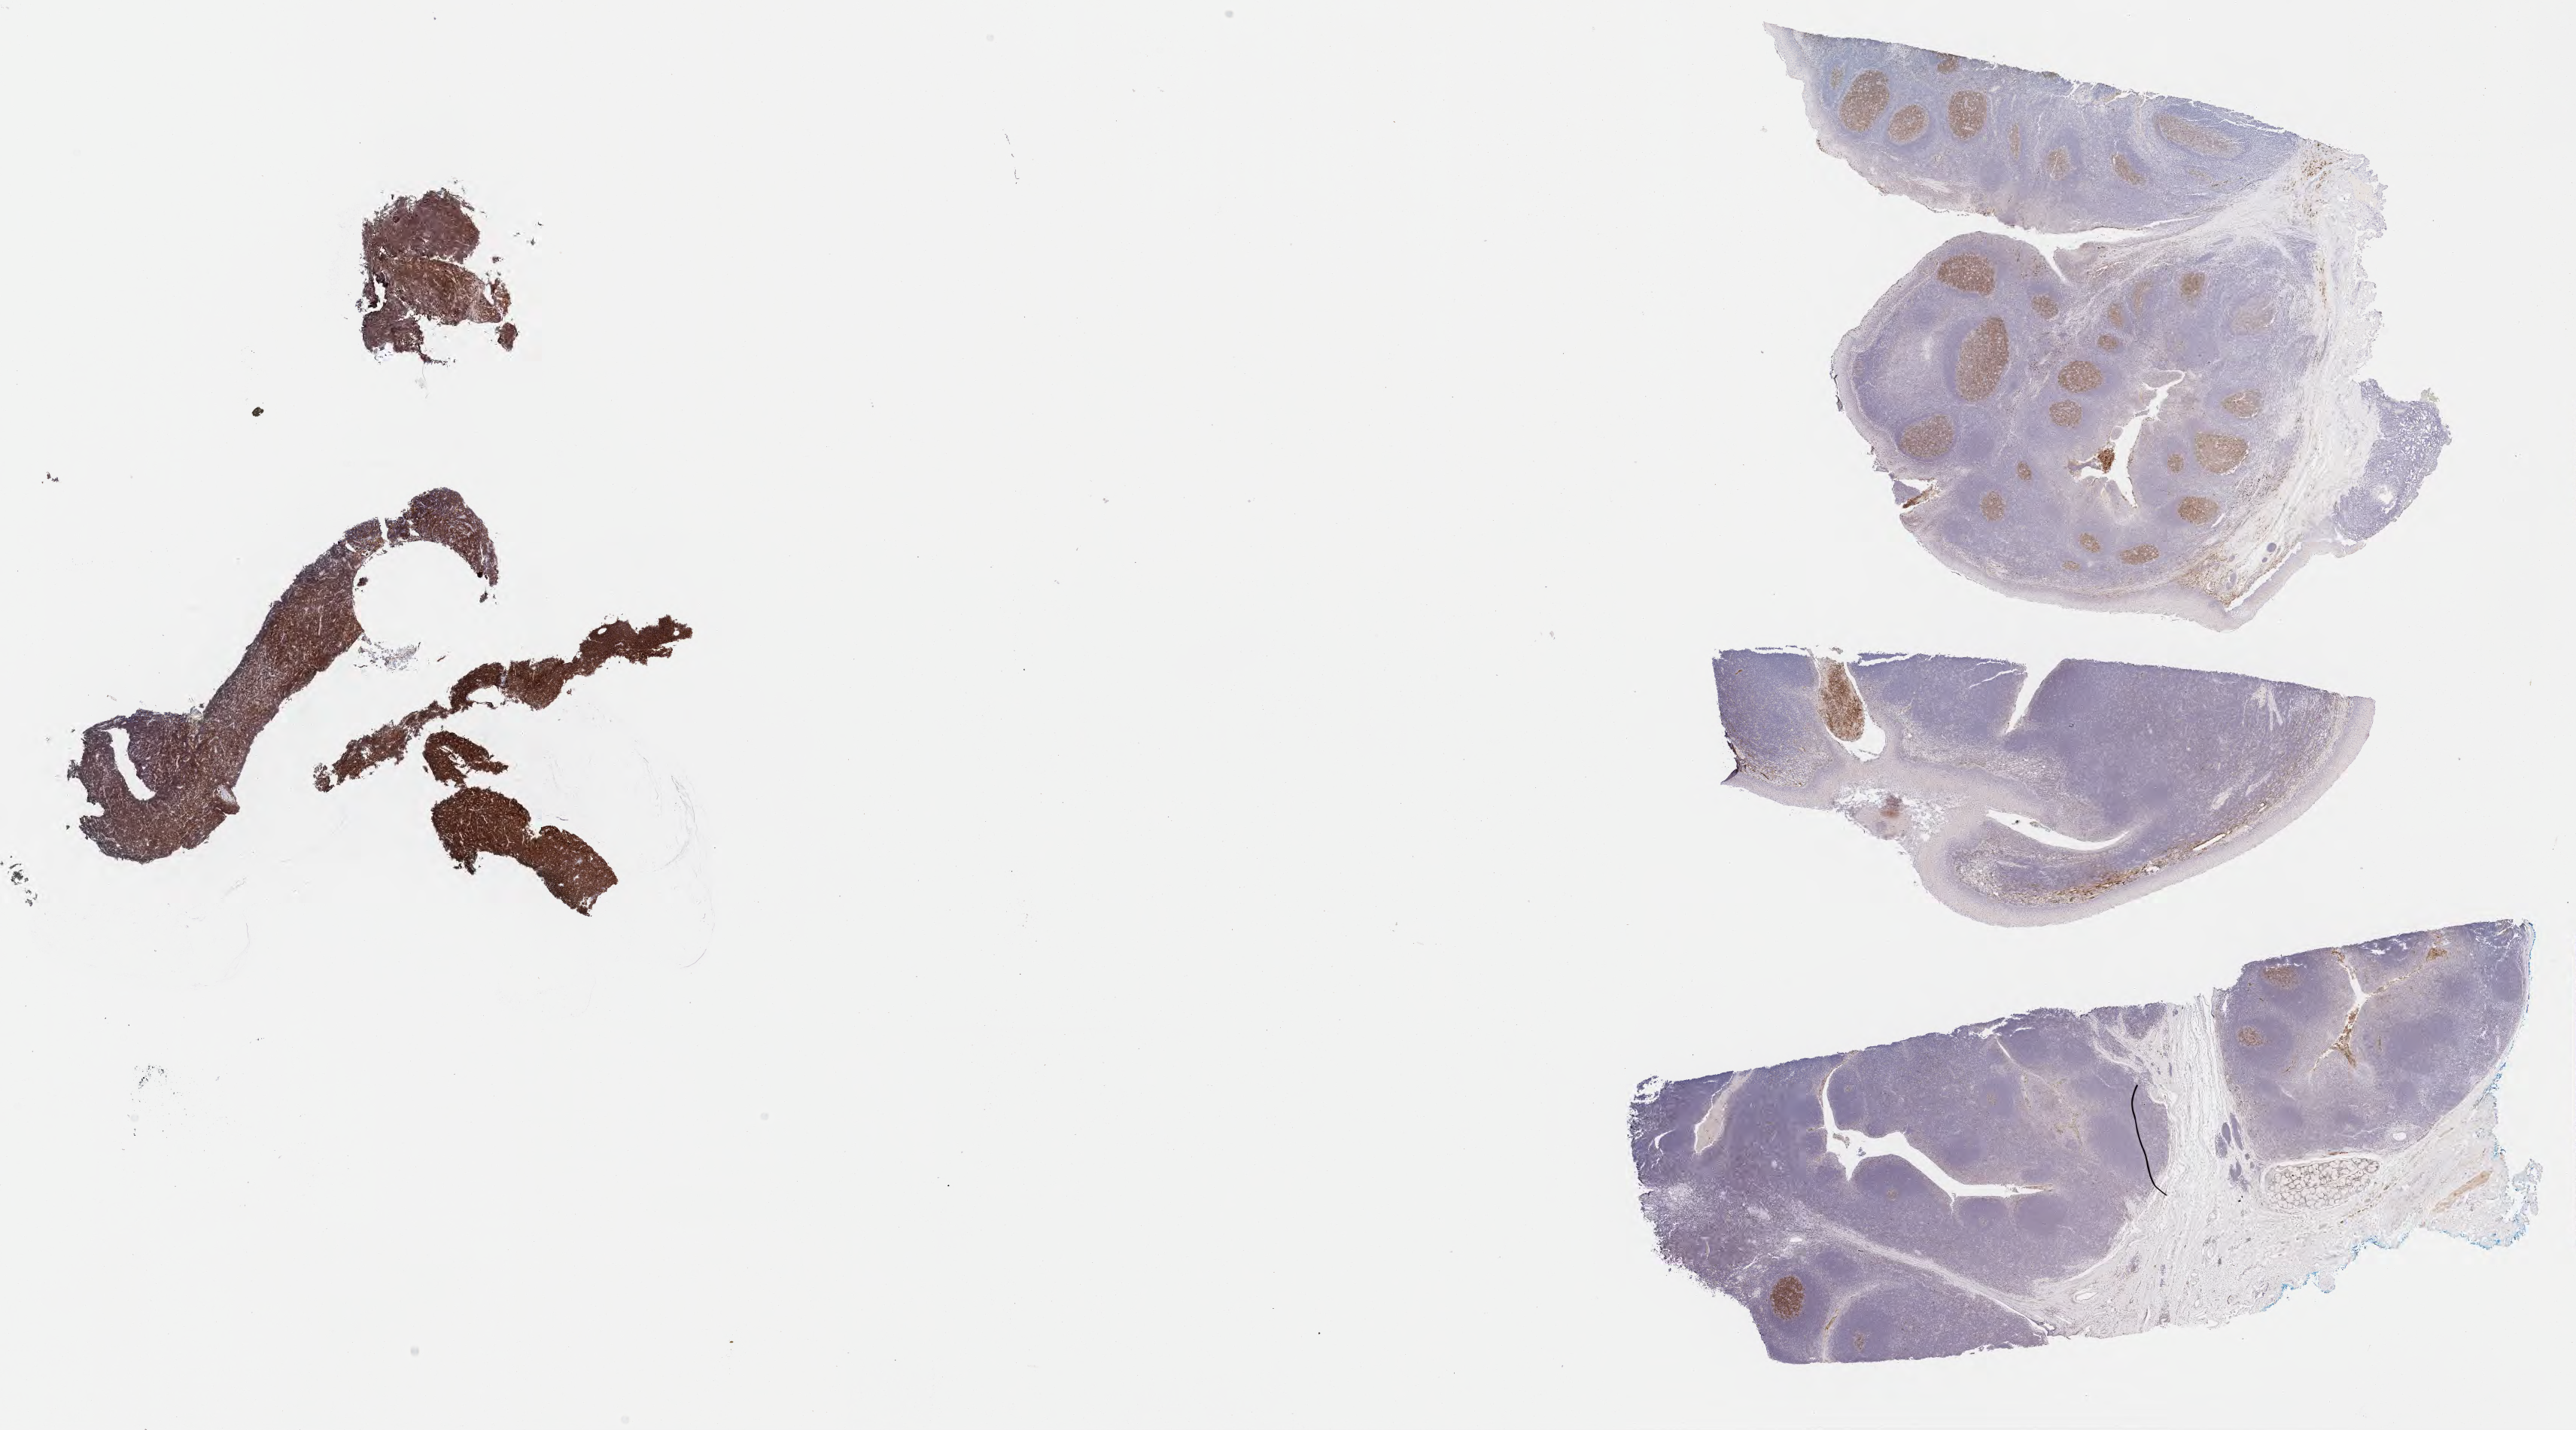
Immunohistochemistry (IHC) whole-slide image stained for CD10 — low-resolution overview of the scanned area, about 27.7 x 15.4 mm; tumor tissue; anatomic site: cranium. Male patient; age at initial diagnosis 5 years.
• histologic diagnosis: Burkitt lymphoma, NOS